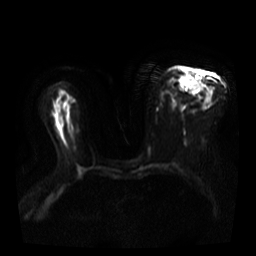
Breast MRI, one axial slice. Slice 20 of 40 in the series (ordered by position). Diffusion-weighted series; image 2 of 4 stored at this slice position (different b-values; order by instance number). 3 T. 5 mm slice thickness. 256 × 256 image matrix, field of view 360 × 360 mm. Female patient.
Structures marked on this image (outlined manually by an expert reader):
- tumour on diffusion-weighted imaging: box from (x=191, y=76) to (x=204, y=85) px